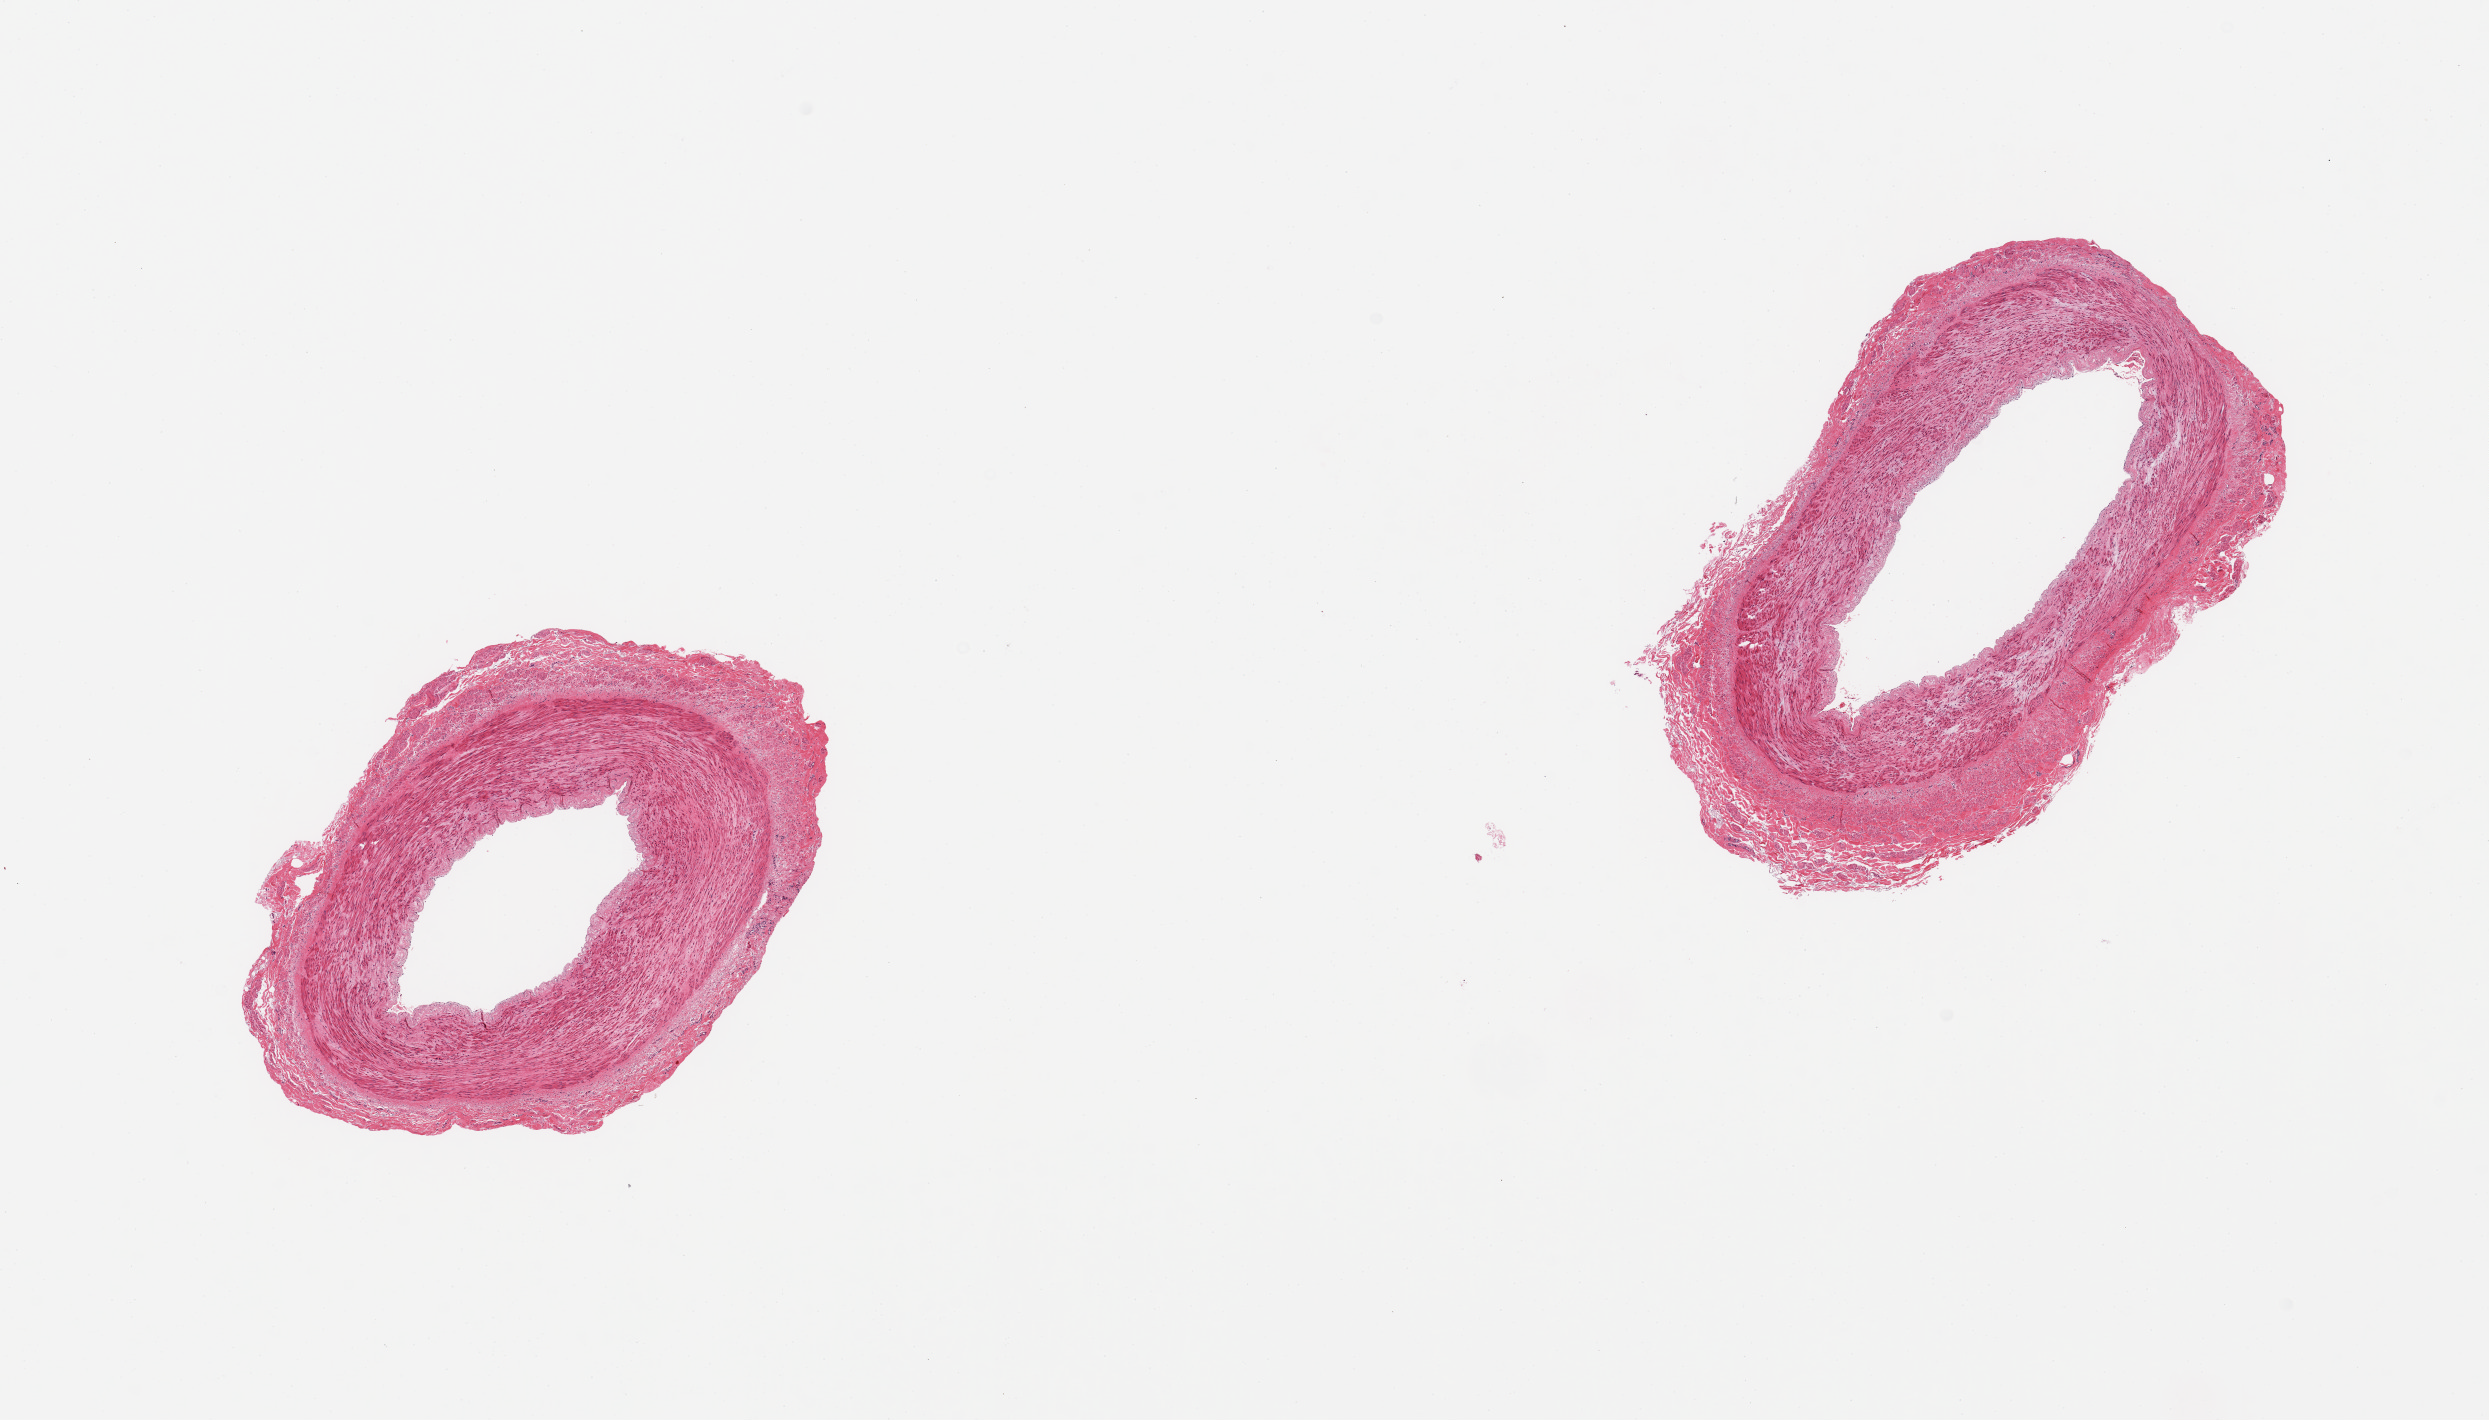
Whole-slide image, hematoxylin and eosin (H&E) stain, whole scanned area (about 19.7 x 11.2 mm) shown as a low-resolution overview. PAXgene-fixed, paraffin-embedded tissue. Target tissue: tibial artery. Tissue donor sample. Female donor.
Review note (as recorded): 2 pieces; well trimmed, no plaques.